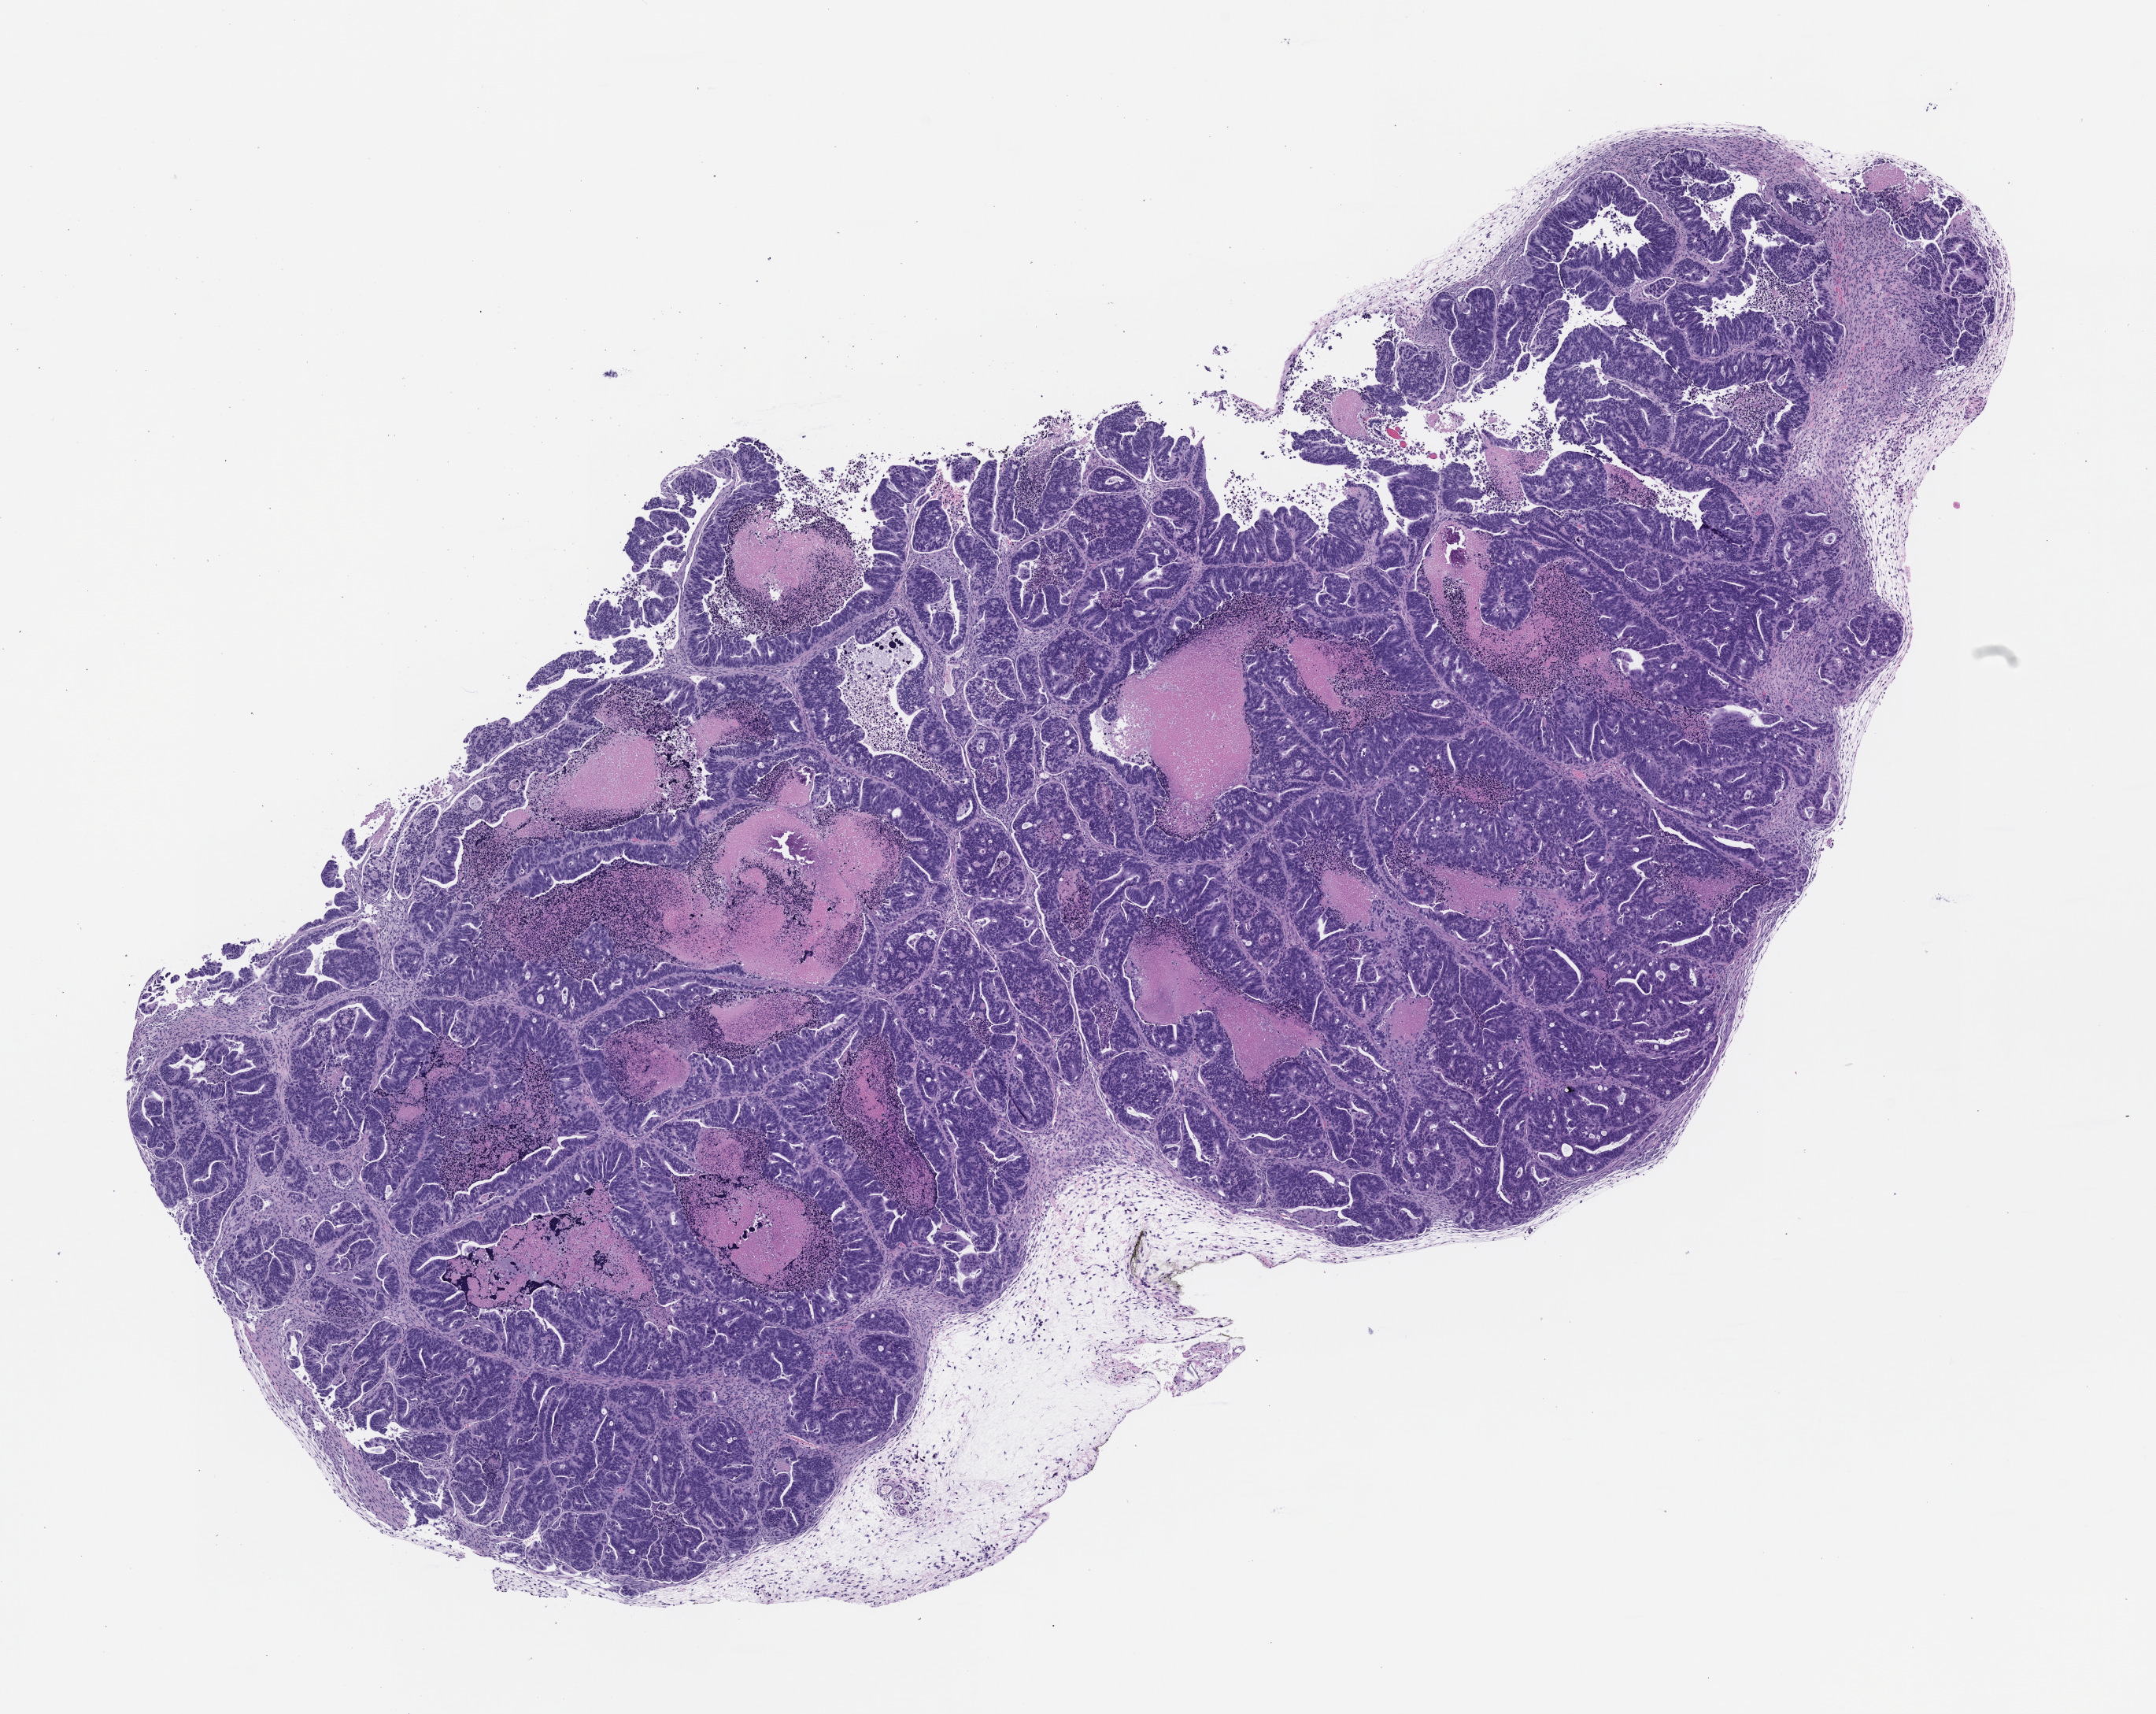
Haematoxylin and eosin whole-slide image of a patient-derived xenograft (PDX) tumor grown in a mouse, passage 0 — low-resolution overview of the scanned area, about 11.0 x 8.8 mm, FFPE section, originating tumor site category: colon.
Originating patient diagnosis: Colon Adenocarcinoma.